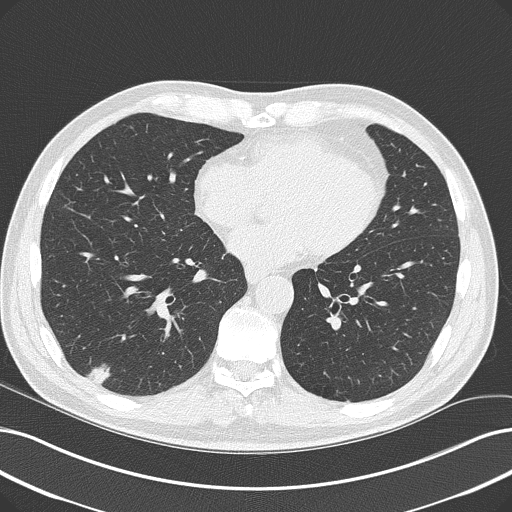
Low-dose screening chest CT, one axial slice; position 93 of 228 along the scan axis; 120 kVp; lung window (W 1500 / L -600 HU); 512 × 512 image matrix, field of view 366 × 366 mm.
Outlined on this slice (expert manual segmentation):
- lesion 1 (tumor, lower lobe of right lung): bounding box <86,365,111,384> (left, top, right, bottom; pixels)